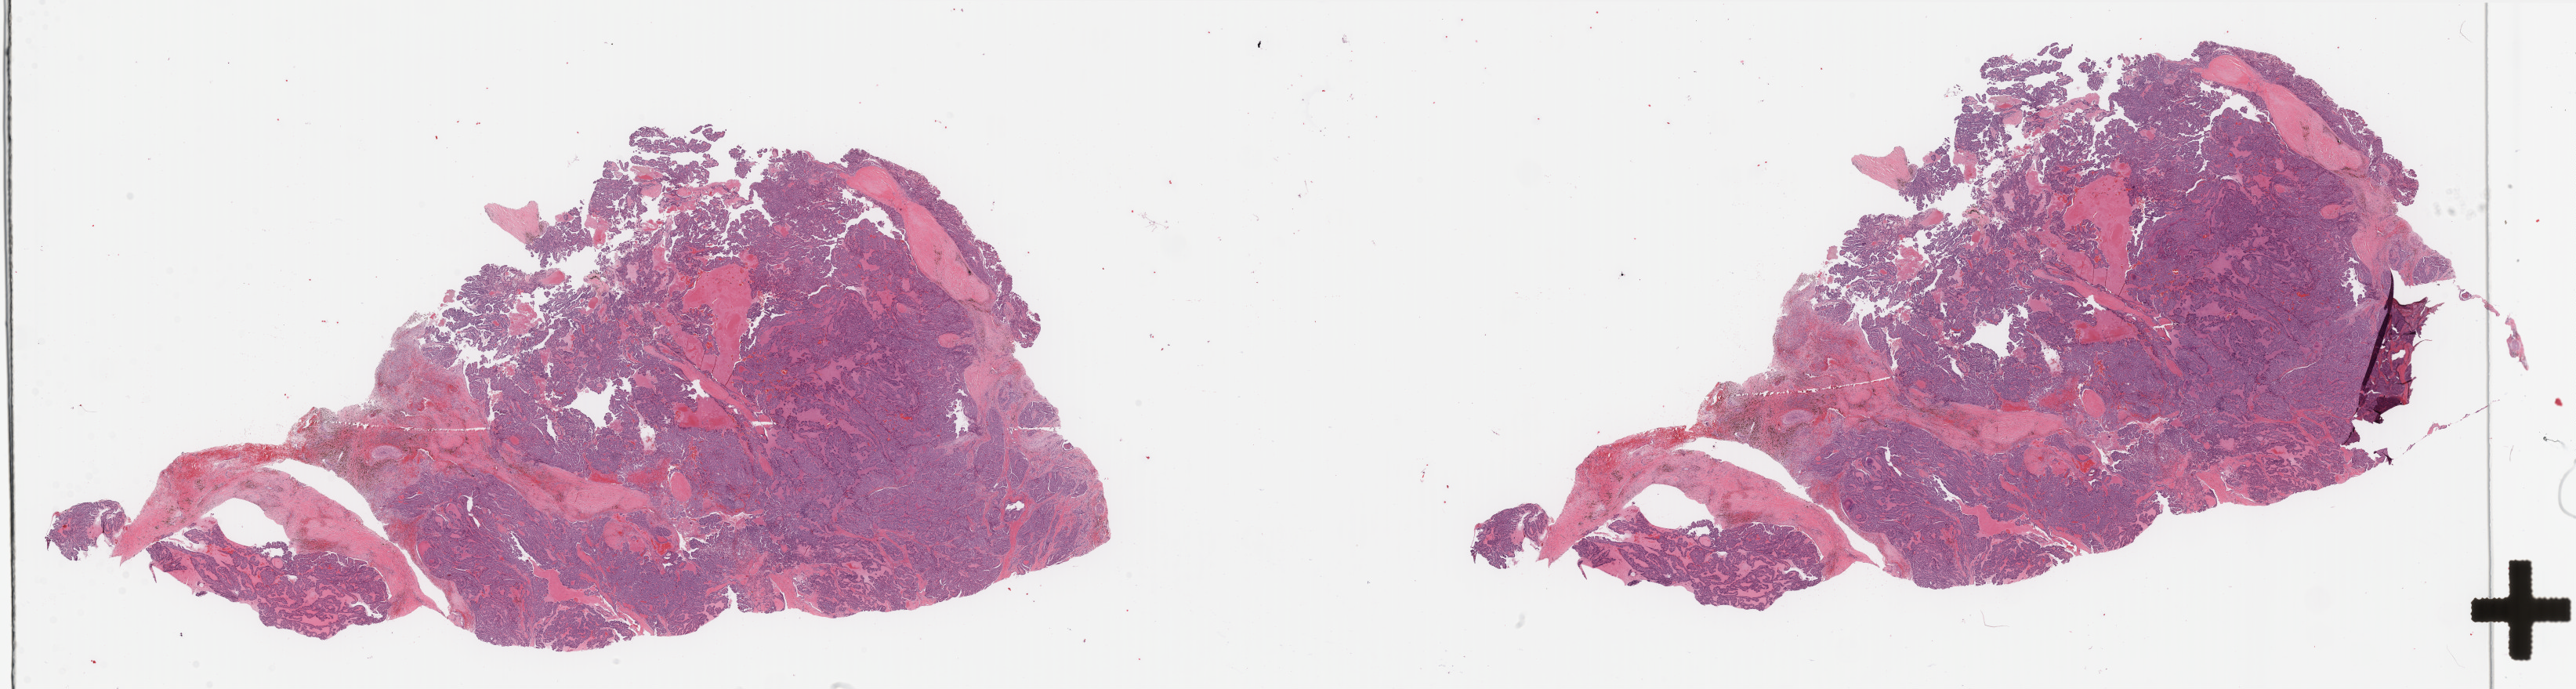
H&E-stained whole-slide image — whole scanned area (about 52.0 x 13.9 mm, acquisition: 40x scan) shown as a low-resolution overview. FFPE section. Sample: primary tumour, thyroid. Male, age 71 years at initial diagnosis.
* lymph nodes positive (case pathology): 9 of 41 examined
* diagnosis: Papillary adenocarcinoma, NOS (thyroid gland)
* AJCC pathologic stage: IVA (7th edition)